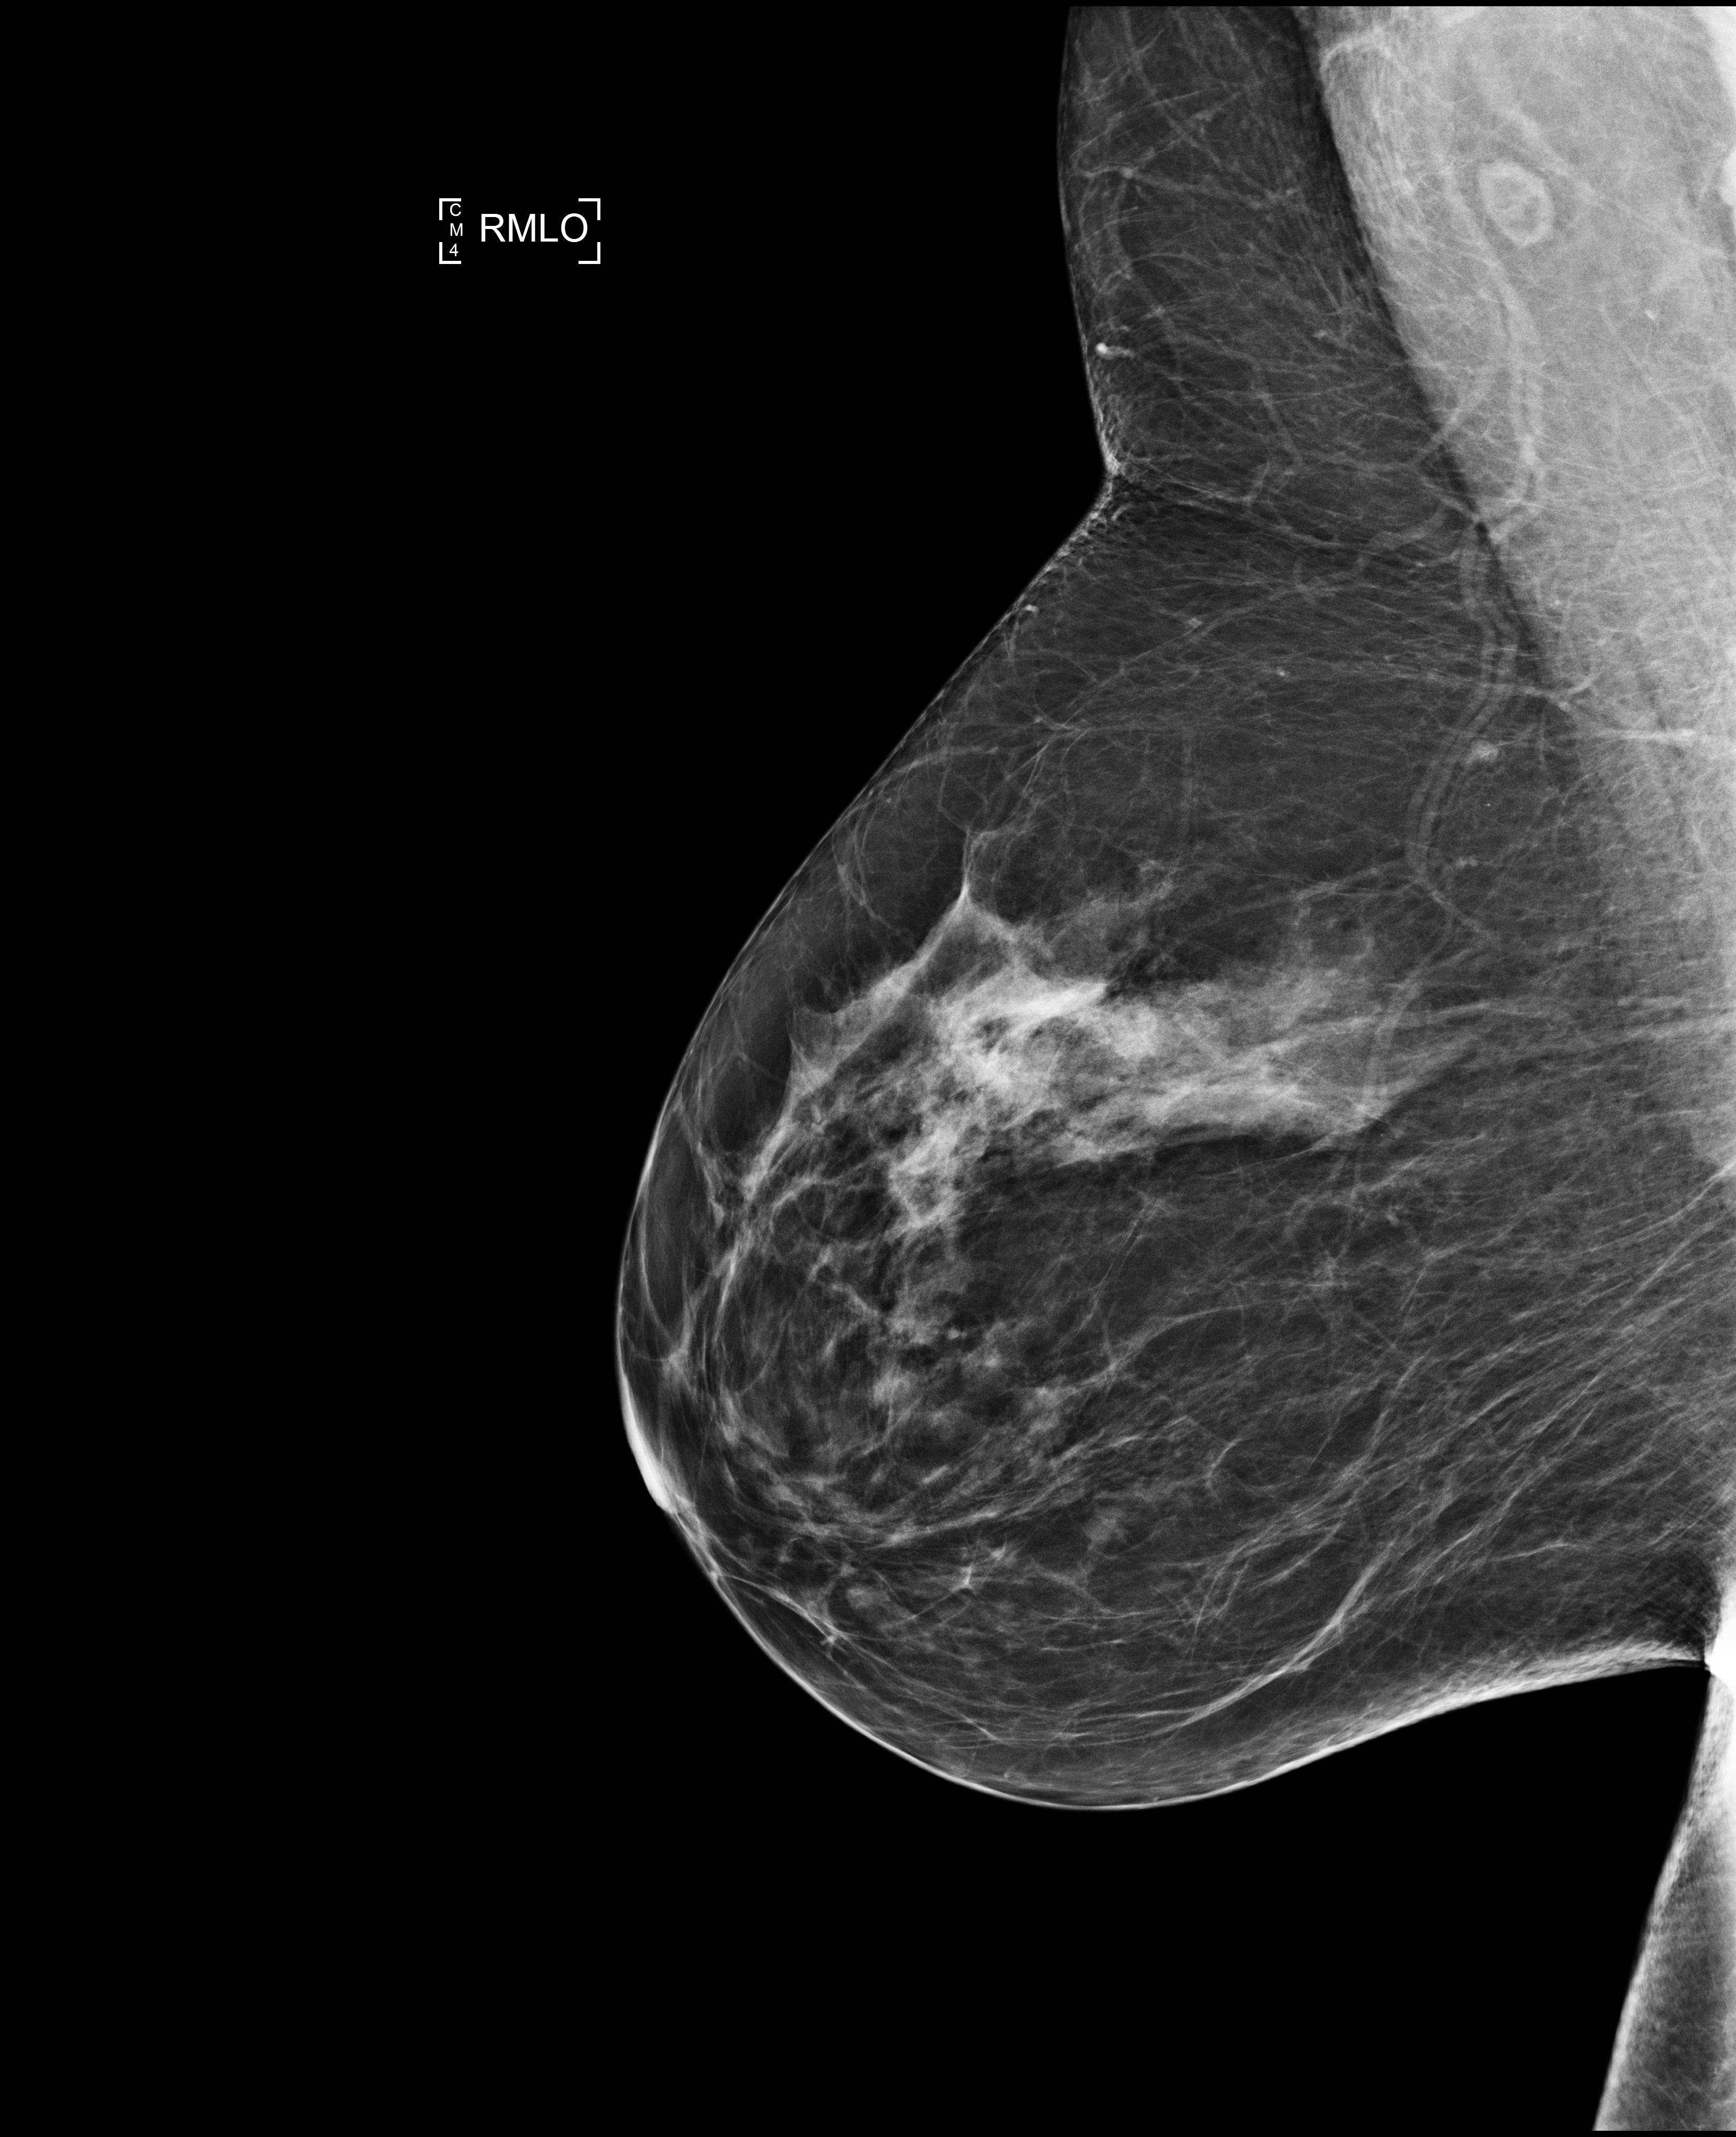
Screening examination; compressed breast thickness 73 mm. Patient: female, 55 years.
Image type: full-field digital mammogram. Breast: right. Projection: medio-lateral oblique projection.